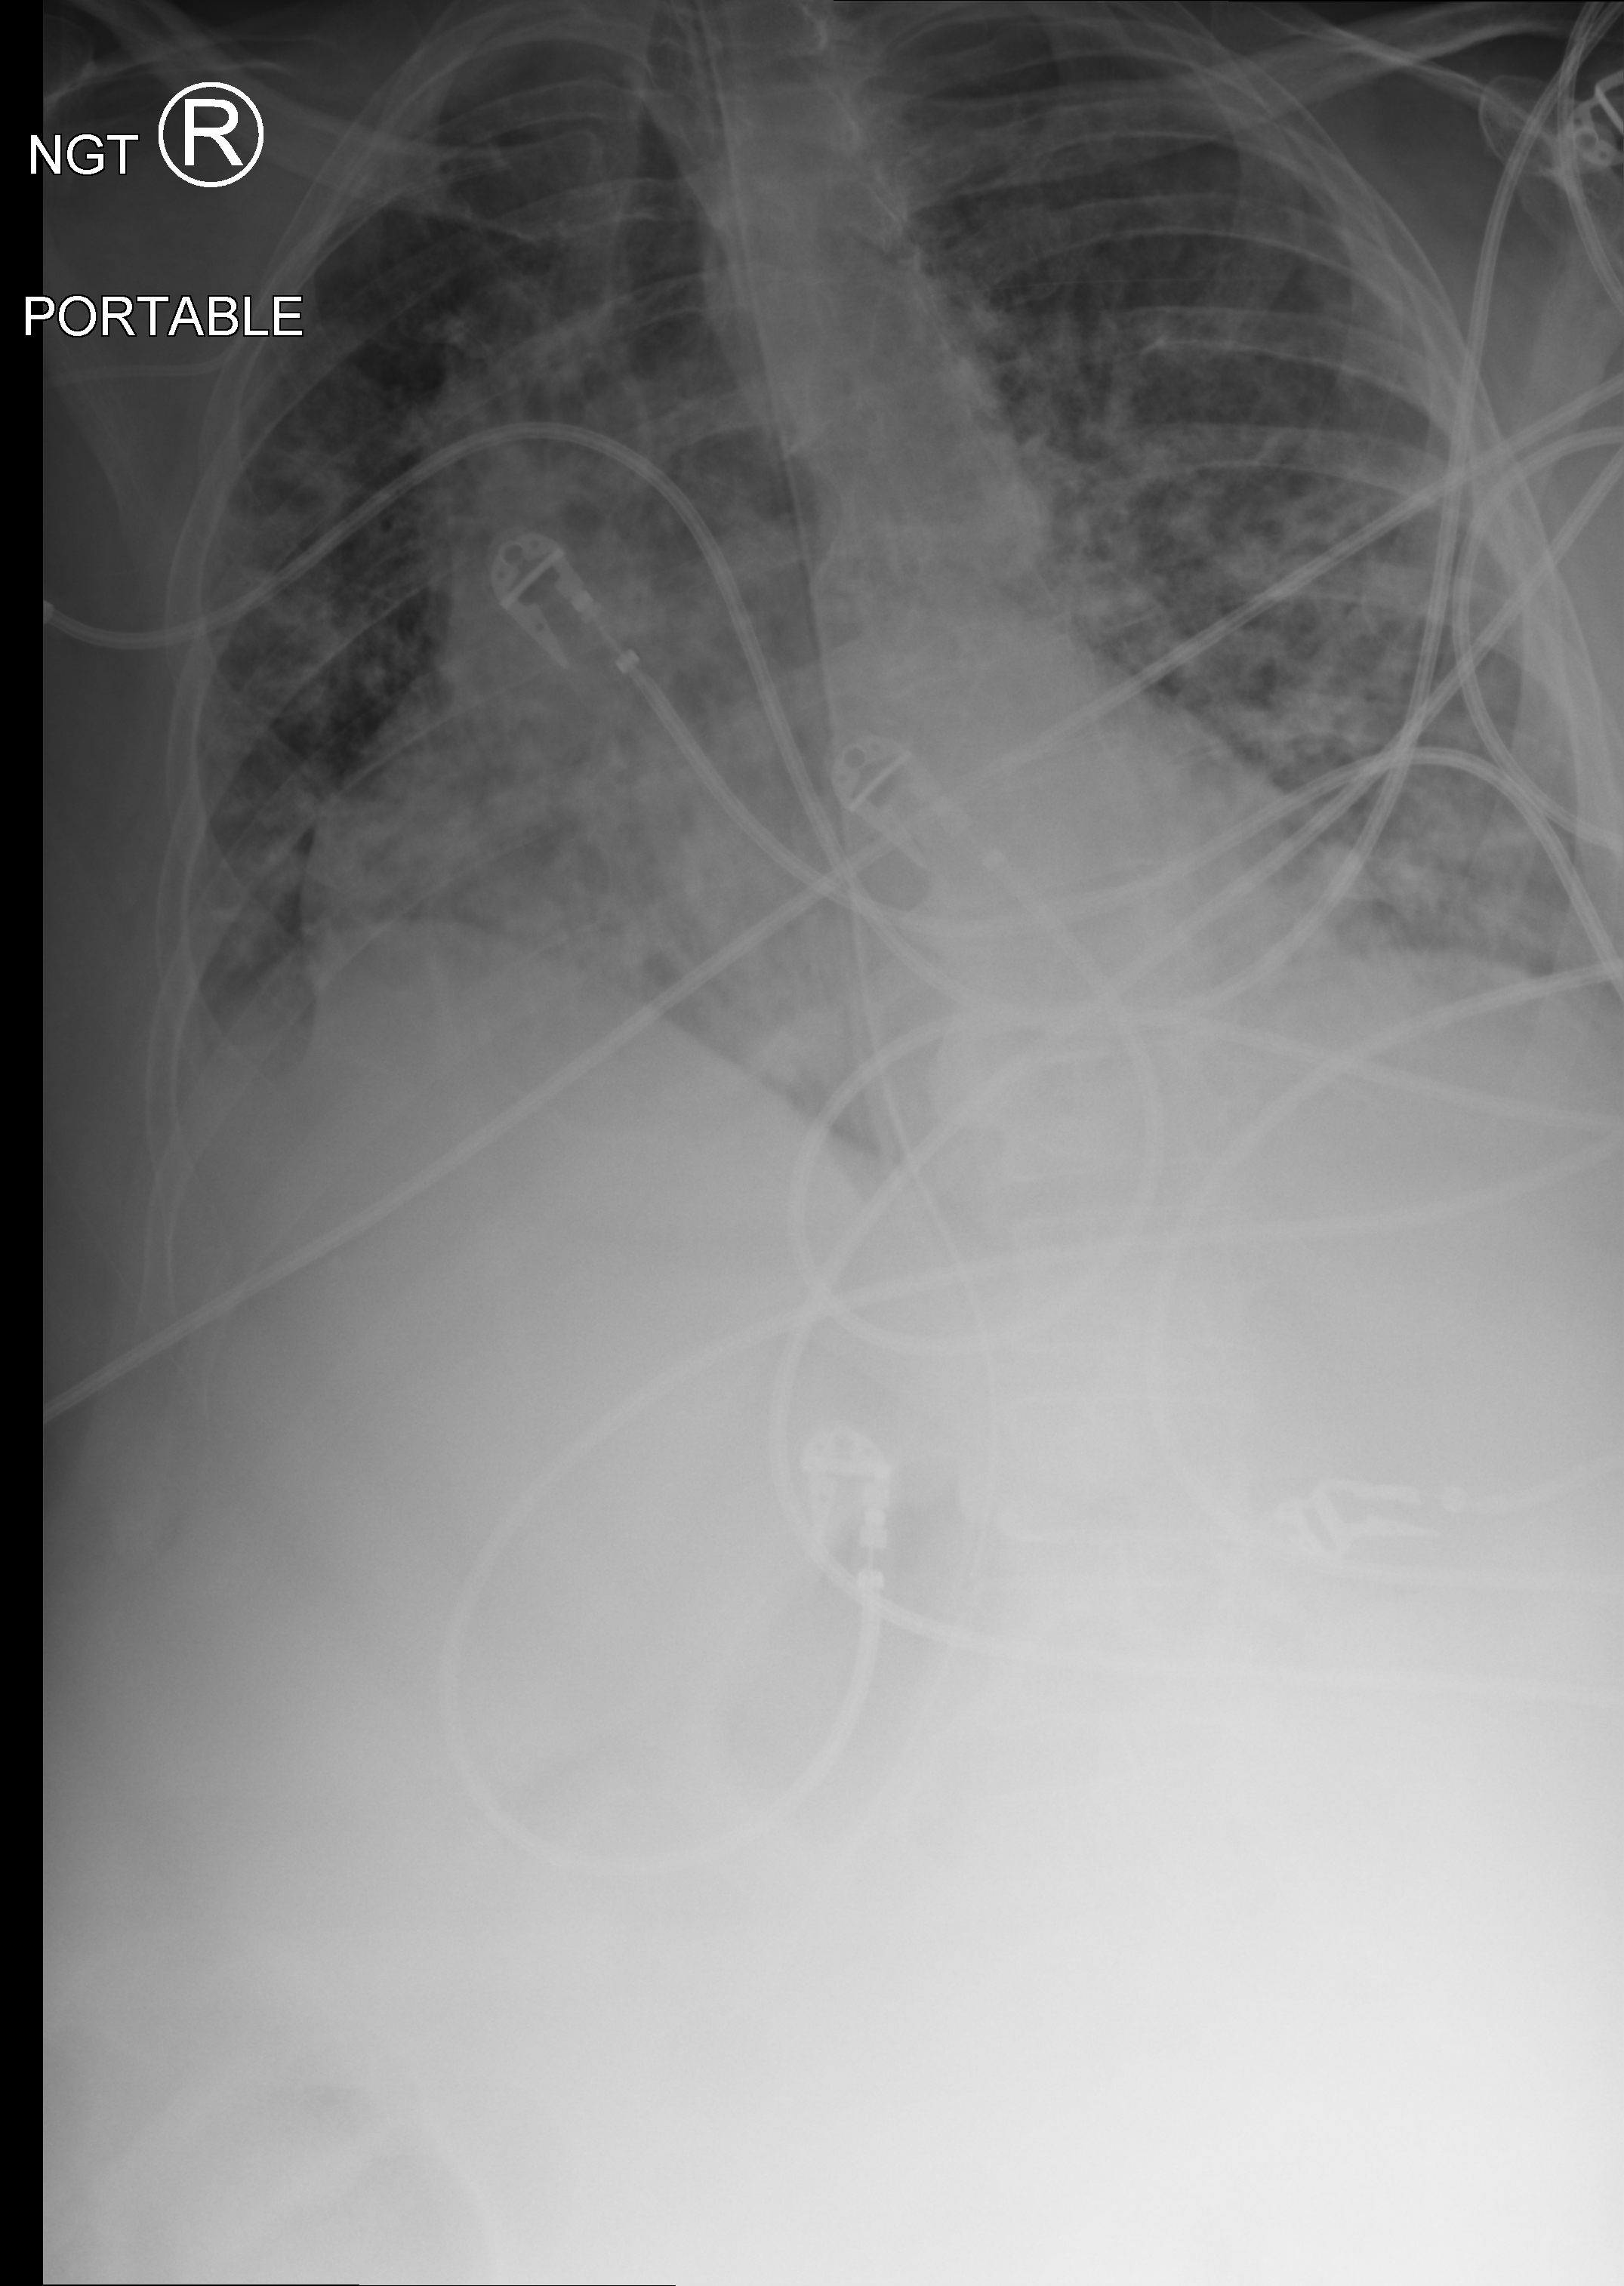
Chest X-ray (portable), anteroposterior (AP) projection. Patient hospitalised with COVID-19; female, aged 75–90 years.
Hospital-stay facts (about this admission, not read from this image; timing relative to this image not recorded): admitted to intensive care during this hospital stay: yes; length of hospital stay: 31 days; hypertension (admission record): yes.